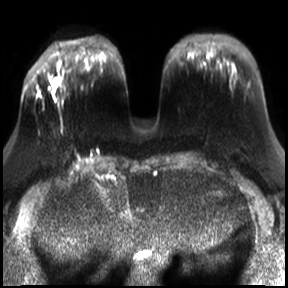
Breast MRI, one axial slice; slice 8 of 30 in the series (ordered by position); diffusion-weighted series; image 2 of 4 stored at this slice position (different b-values; order by instance number); 3 T; 4 mm slice thickness; 288 × 288 image matrix. Female patient.
Outlined on this slice (manually delineated by an expert):
- tumour on diffusion-weighted imaging: bounding box (x1, y1, x2, y2) in pixels: (53, 78, 57, 85)